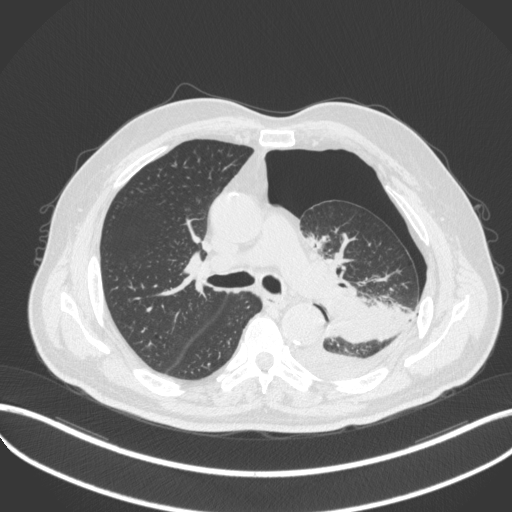
Chest CT, one axial slice; position 324 of 466 along the scan axis; reconstruction kernel B31f; lung window (W 1500 / L -600 HU); 1 mm slice thickness; 512 × 512 image matrix, field of view 400 × 400 mm. Male patient, age 76 years. Case-level facts recorded for this patient, not image findings: clinical TNM (as recorded): T3 N0 M1b.
Annotated regions visible in this slice (rectangle marked by the reading radiologist):
- lung tumour (recorded histology: adenocarcinoma): bounding box [x1, y1, x2, y2] px = [323, 289, 396, 340]